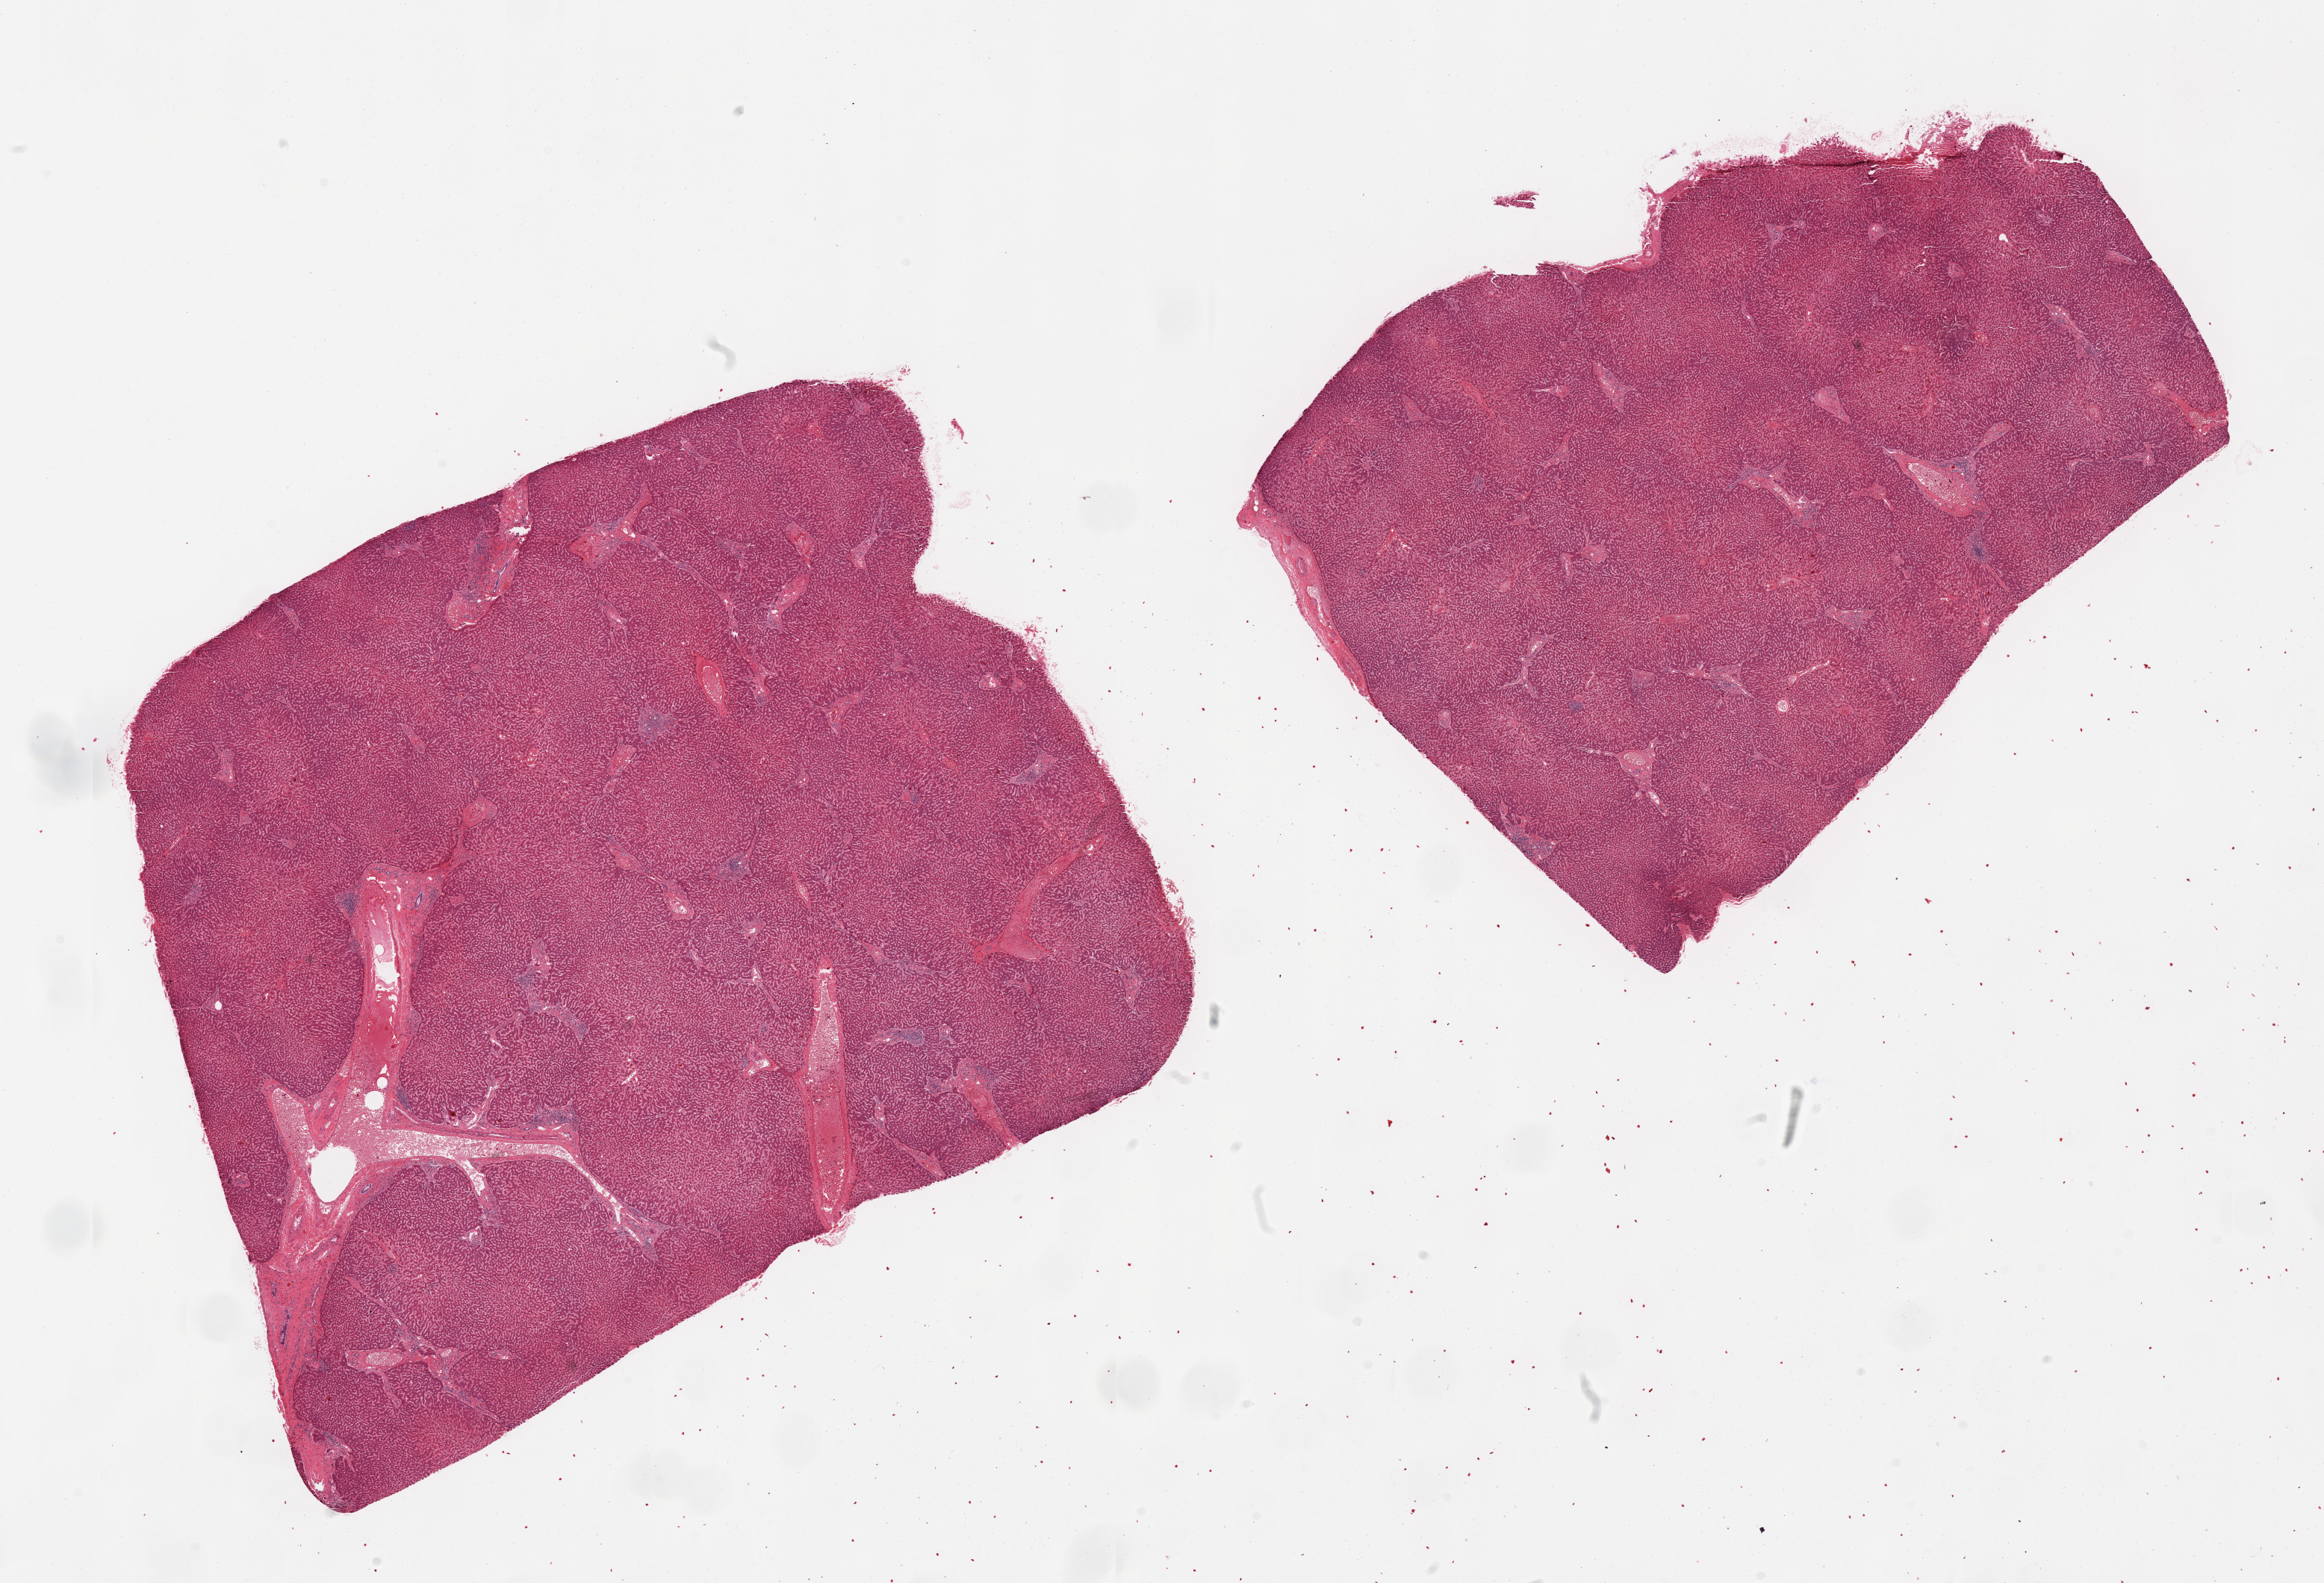
Whole-slide image, haematoxylin and eosin stain, a low-resolution overview of the entire scanned area, about 24.6 x 16.8 mm (slide scanned at 20x); PAXgene-fixed, paraffin-embedded tissue; section of liver (target tissue); tissue donor sample. Donor: male.
Pathologist's review note for this sample: 2 pieces, mild congestion, mild chronic hepatitis. No significant steatosis.